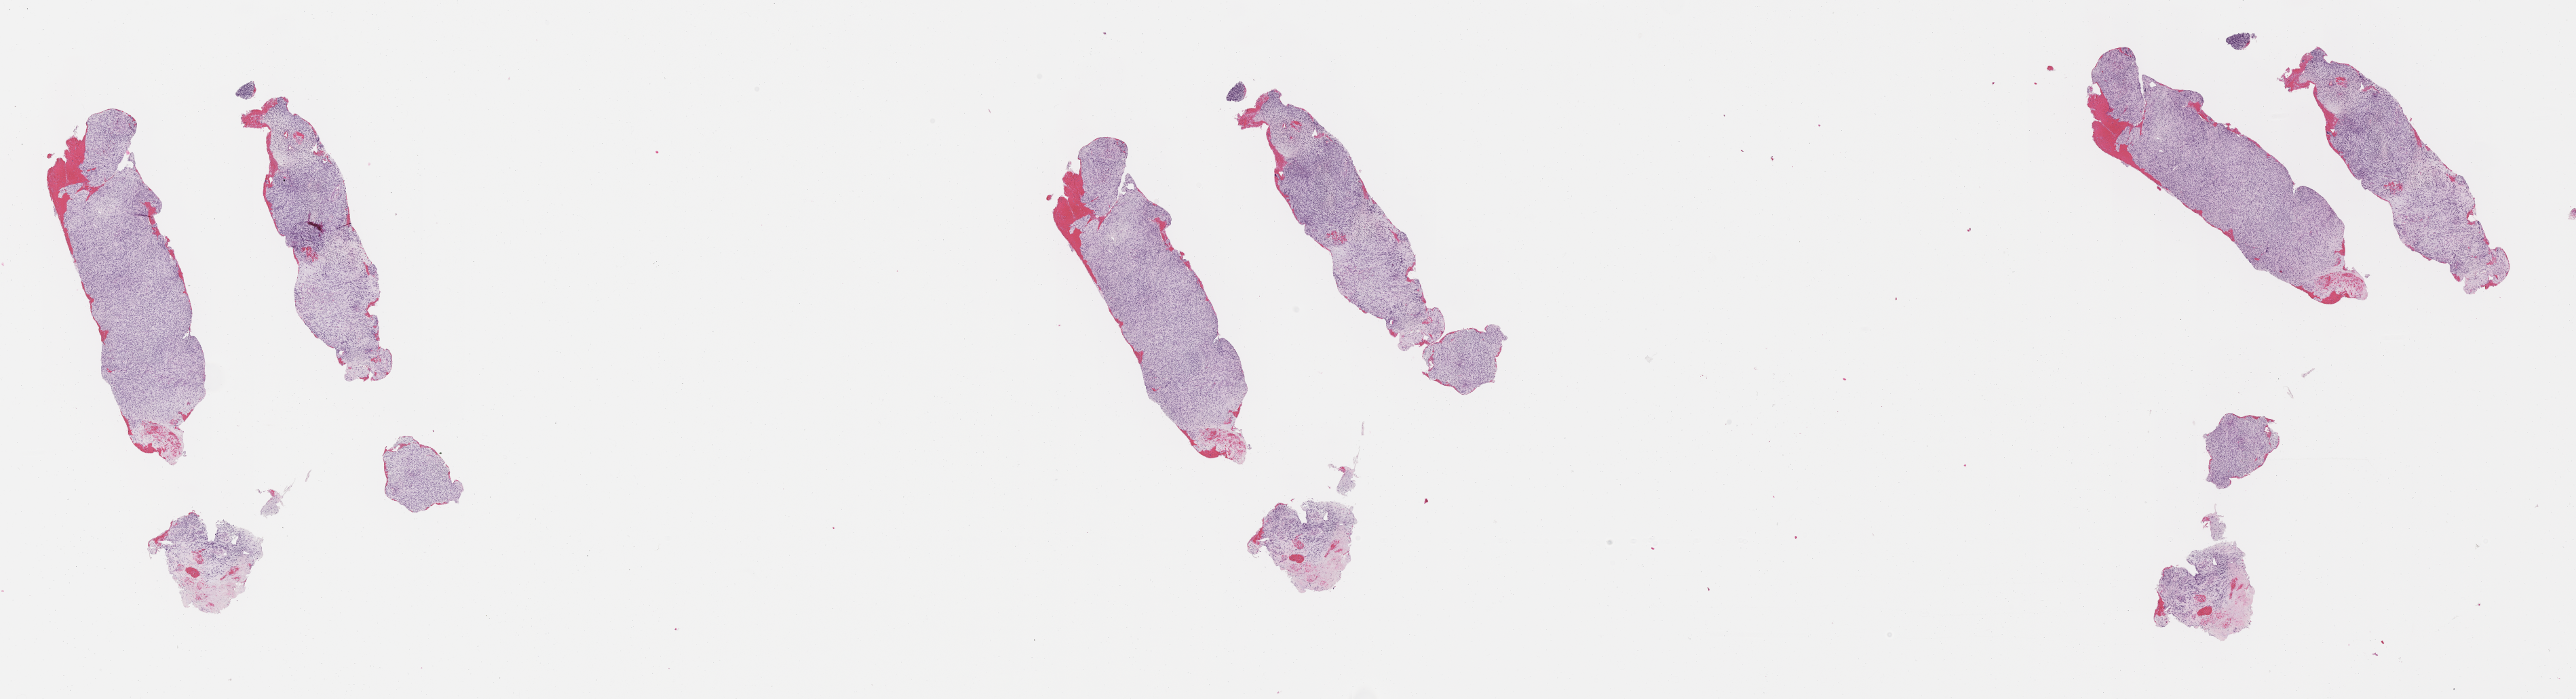
Whole-slide image, haematoxylin and eosin stain of tumor tissue — a low-resolution overview of the entire scanned area, about 30.7 x 8.3 mm, FFPE section. Male patient, age at diagnosis 2.9 years.
Diagnosis: rhabdomyosarcoma; histological classification: spindle cell rhabdomyosarcoma. Metastatic status at presentation (as recorded): non-metastatic. Stage (as recorded): 3.